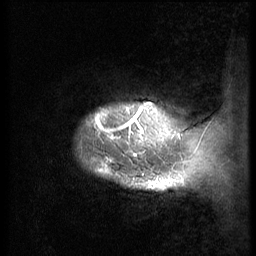
Breast MRI (dynamic contrast-enhanced), one sagittal slice. Slice 4 of 56 in the series (ordered by position). 3 images stored at this slice position (order not interpretable as contrast timing). 1.5 T. TE 4.2 ms, TR 9 ms. 2.5 mm slice thickness. 256 × 256 image matrix. Patient: female, 49 years. From the clinical record (not read from this slice): setting: breast cancer imaged before/during neoadjuvant chemotherapy; receptor status: HER2-positive.
Outlined on this slice (semi-automatic segmentation, software-assisted and operator-edited):
- analysis volume of interest (the breast-tissue region the enhancement analysis was run in; not a lesion): bounding box (x1, y1, x2, y2) in pixels: (67, 85, 168, 207)
- tumour enhancement mask (voxels above the 140 % enhancement threshold inside the analysis volume of interest): (95, 103, 152, 177)